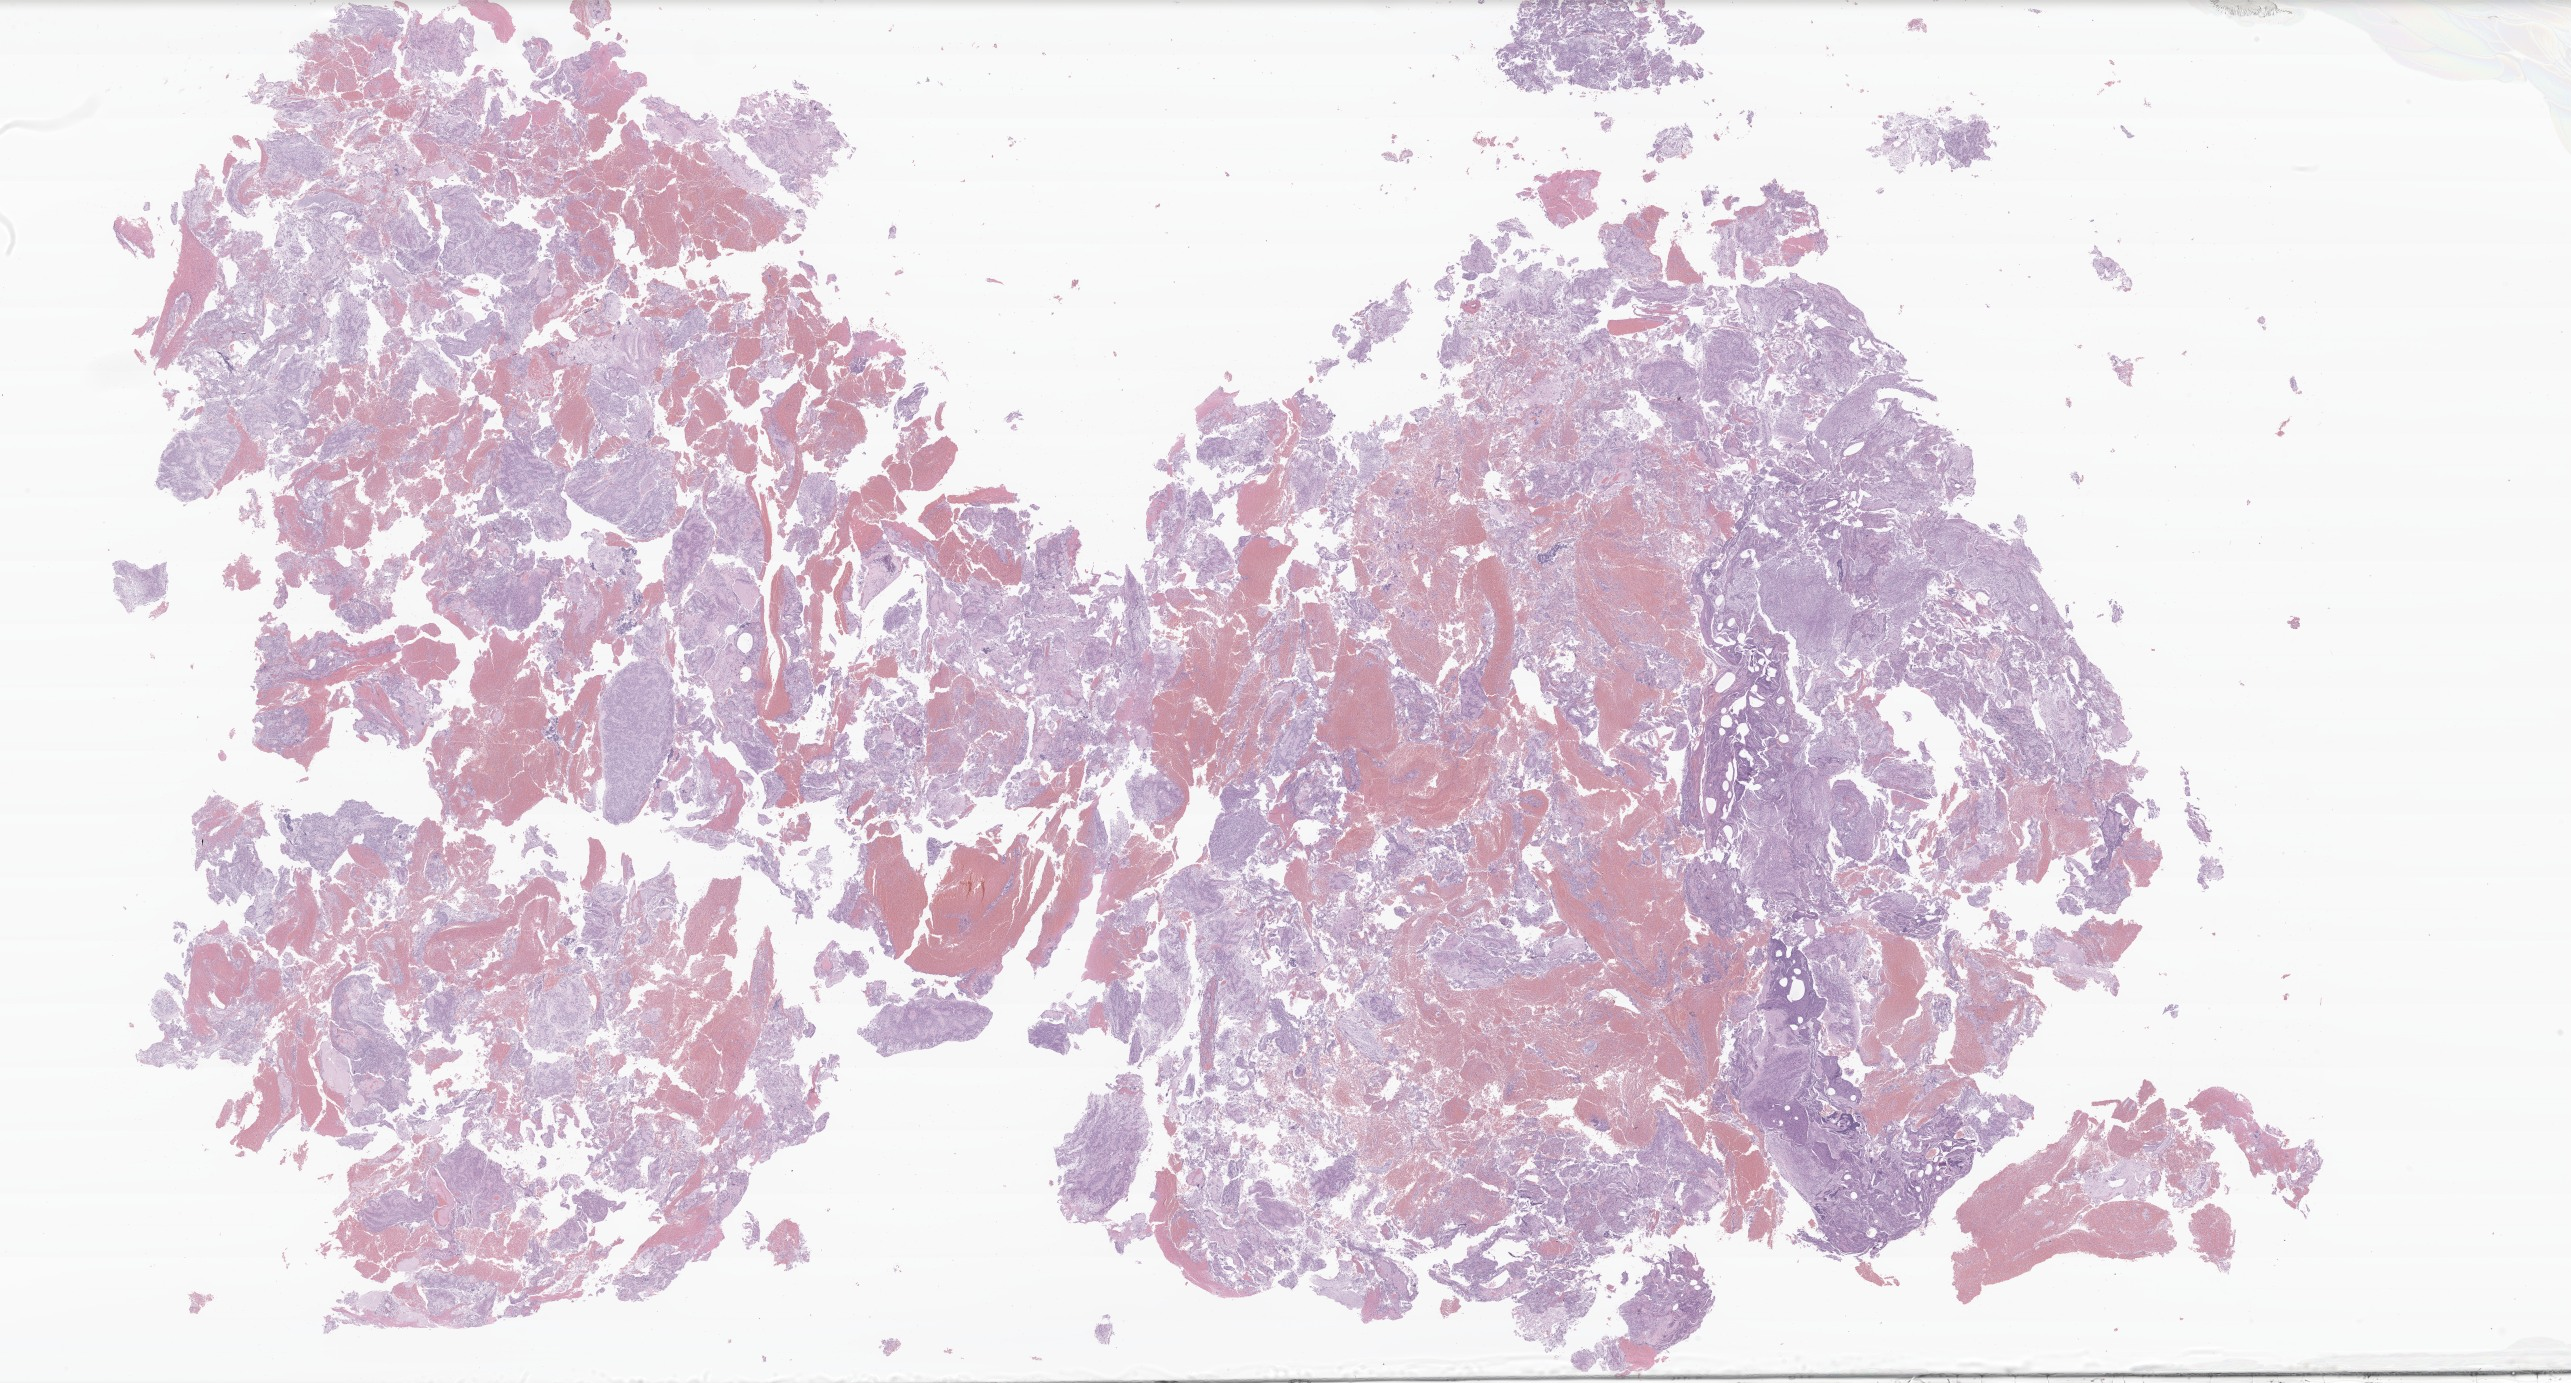
Whole-slide image, hematoxylin and eosin (H&E) stain of tumor tissue from the central nervous system — low-resolution overview of the scanned area, about 43.3 x 23.3 mm; formalin-fixed, paraffin-embedded (FFPE) tissue. Patient male; age 87 months (7 years 3 months).
Diagnosis: Ependymoma, NOS.